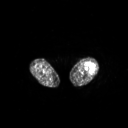
FDG PET of an extremity soft-tissue mass (from a PET/CT study), one axial slice; slice 197 of 267 in the series (ordered by position); 3.27 mm slice thickness; 128 × 128 image matrix, field of view 700 × 700 mm. Female patient, age 62 years. Case-level facts recorded for this patient, not image findings: histological type: undifferentiated – high grade; grade: high; site of the primary tumour: left thigh.
Outlined on this slice (expert contour drawn on MRI and transferred to this co-registered scan by the dataset authors):
- gross tumour volume including surrounding oedema: box from (x=84, y=62) to (x=95, y=72) px